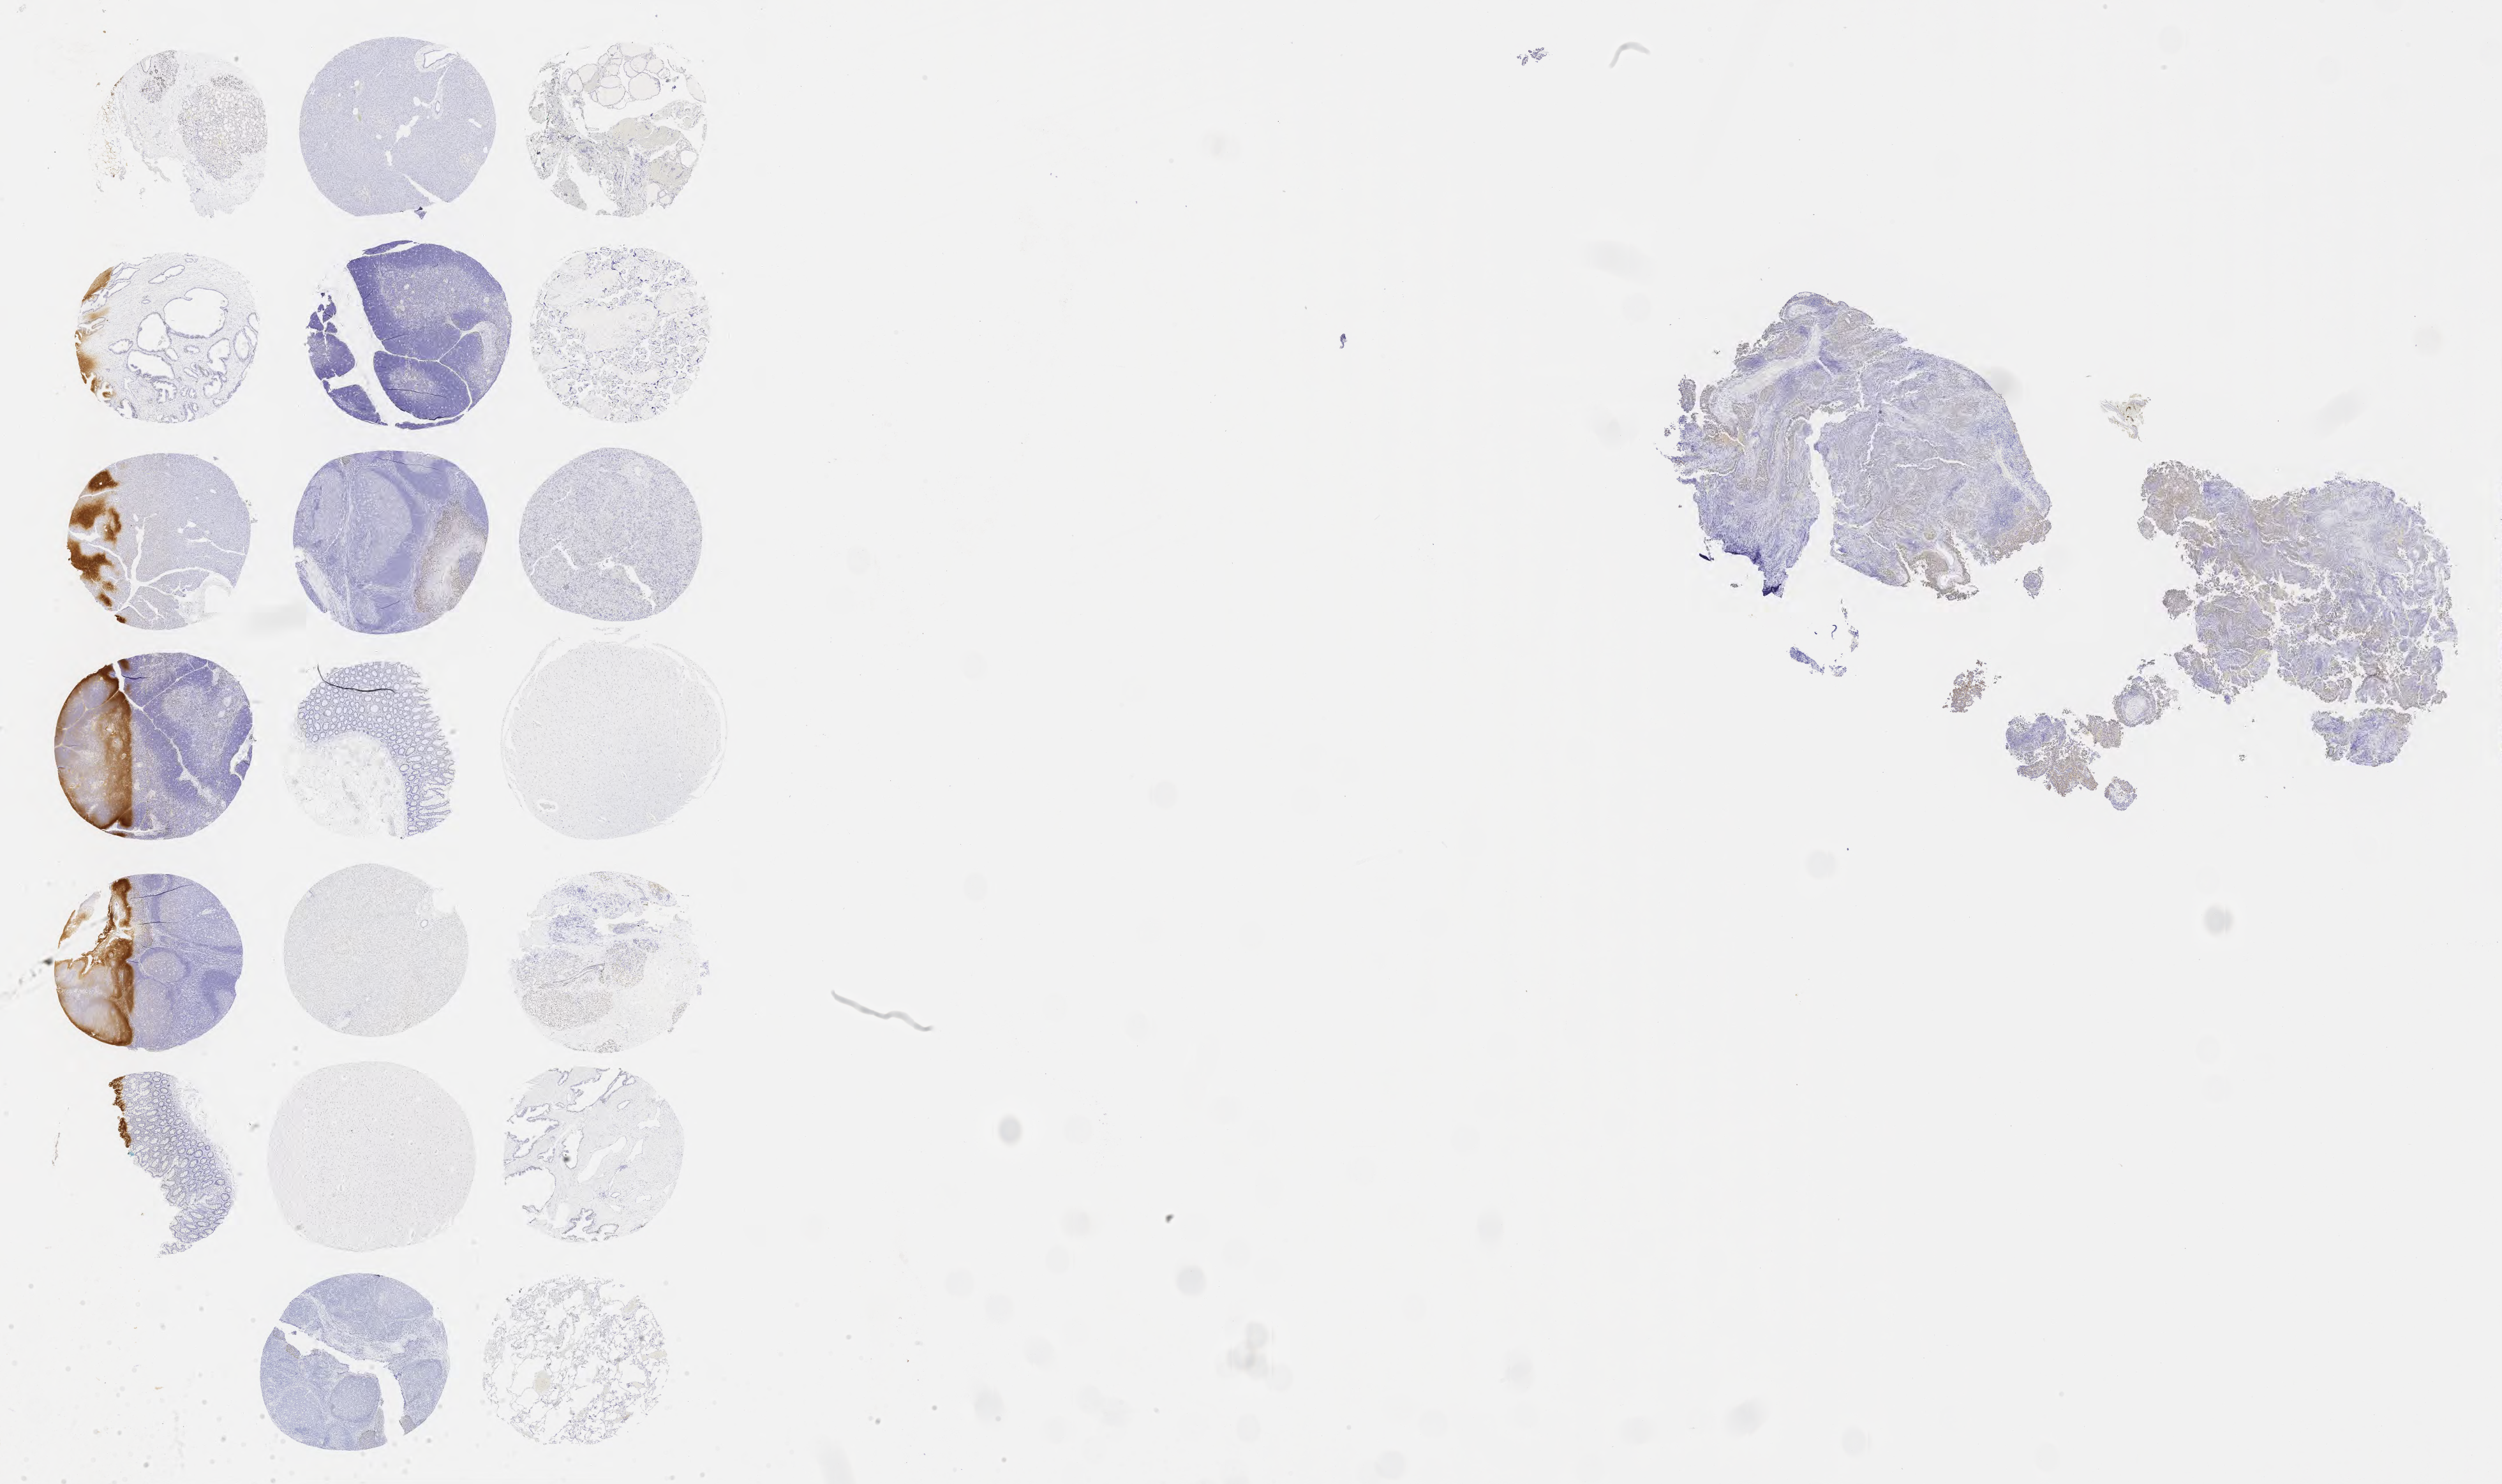
IHC for p63, whole-slide image — shown as a low-resolution overview of the whole scanned area (about 31.7 x 18.8 mm). Tumor tissue. Site: cervix. Patient female; 65 years old.
Histologic diagnosis: Squamous cell carcinoma, large cell, nonkeratinizing, NOS.